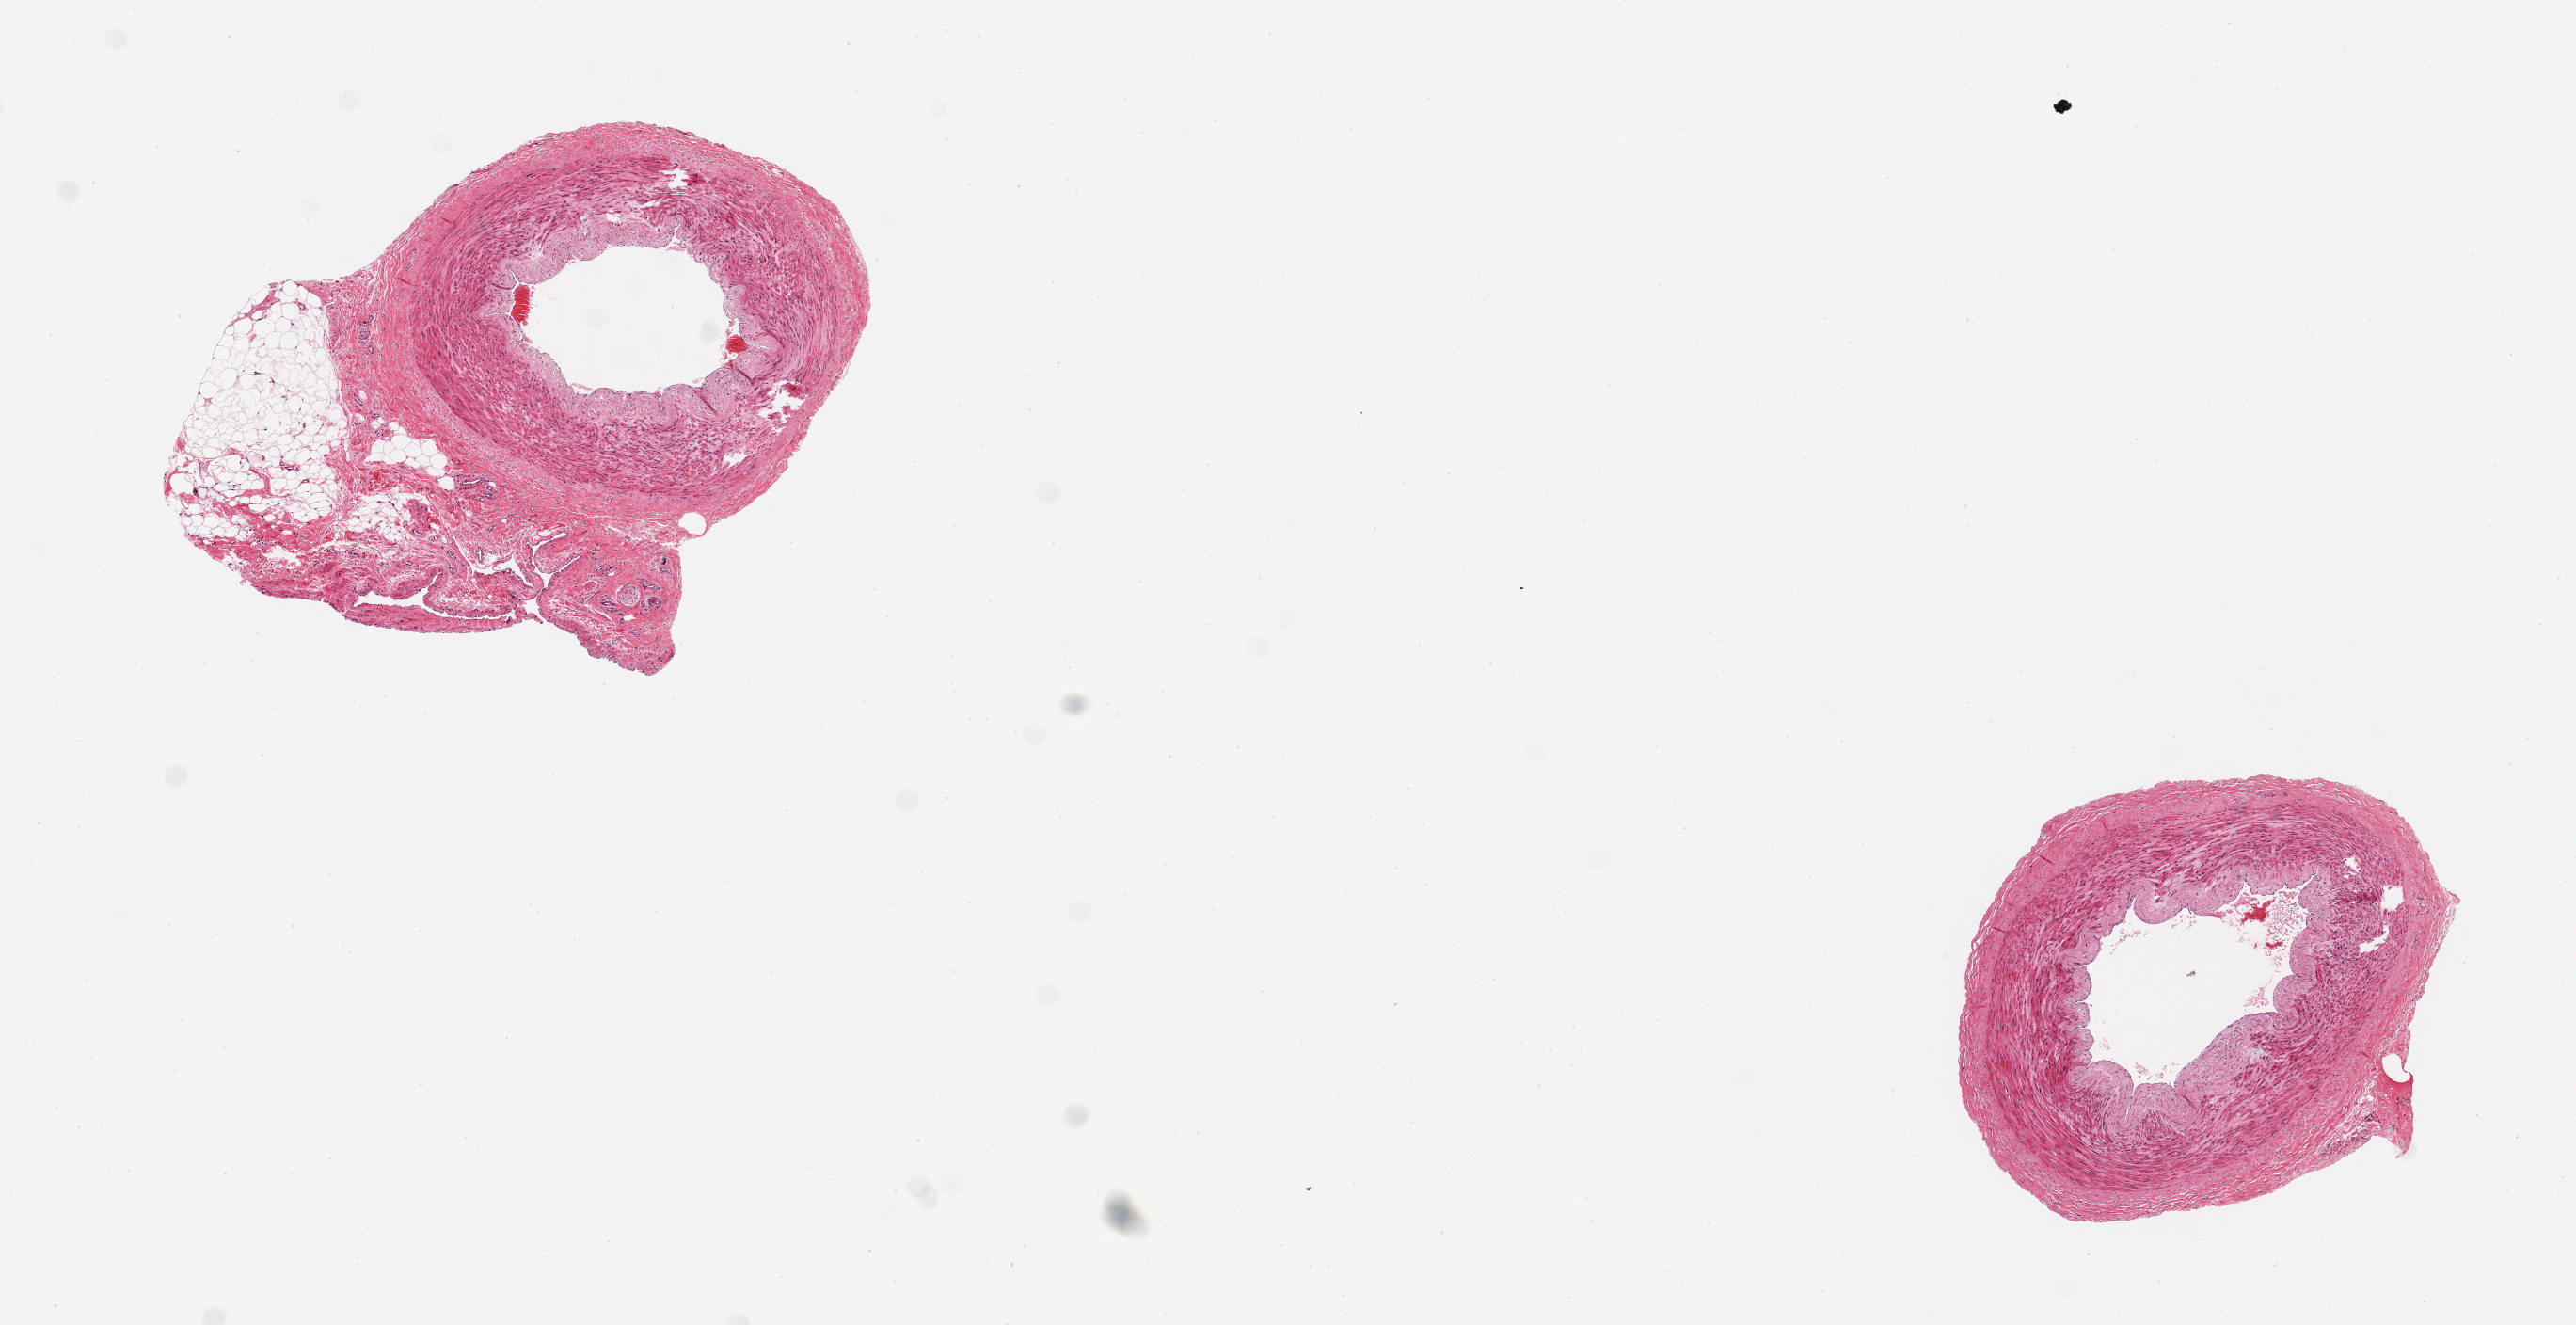
Hematoxylin and eosin (H&E) whole-slide image — a low-resolution overview of the entire scanned area, about 10.8 x 5.6 mm (acquisition: 20x scan); PAXgene-fixed, paraffin-embedded tissue; target tissue: tibial artery; donor tissue sample. Male donor.
Pathologist's review note for this sample: 2 pieces, 2 mm artery; one clean, other ~40% fibroadipose peripherally.